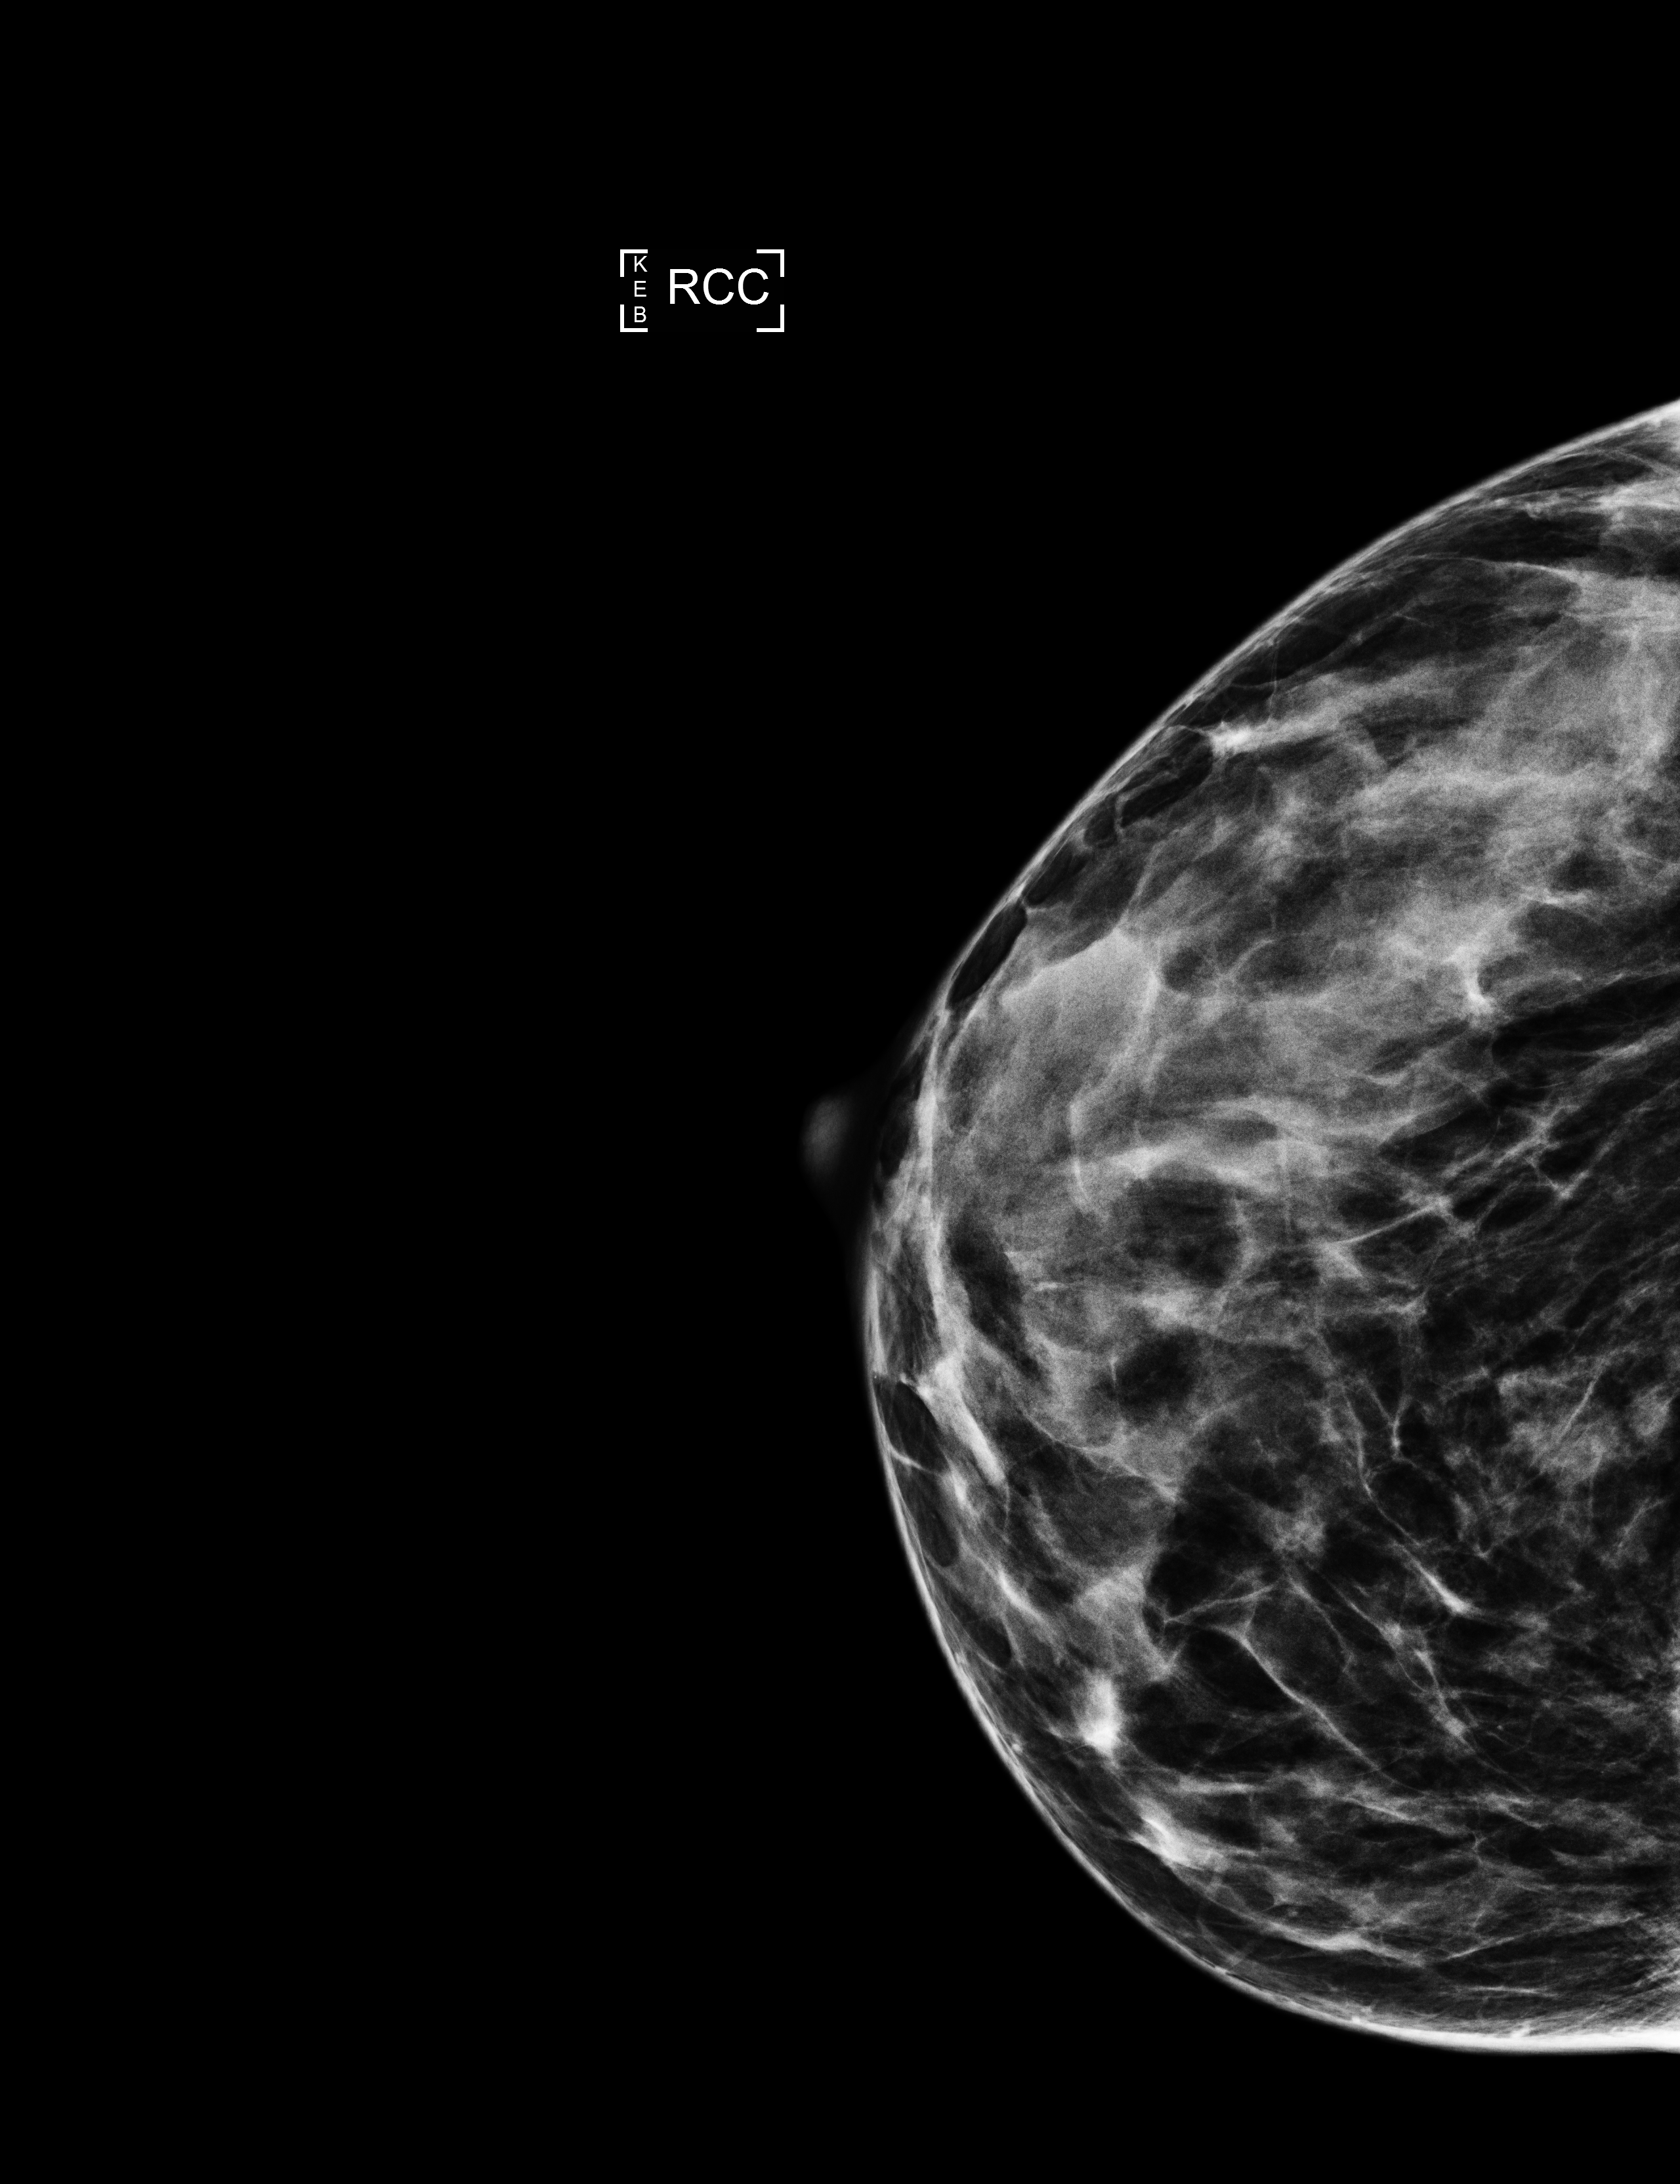
Diagnostic examination (additional views), compressed breast thickness 44 mm, system: Selenia Dimensions. Patient: female, 56 years.
Image type: full-field digital mammogram. Breast: right. Projection: CC view.